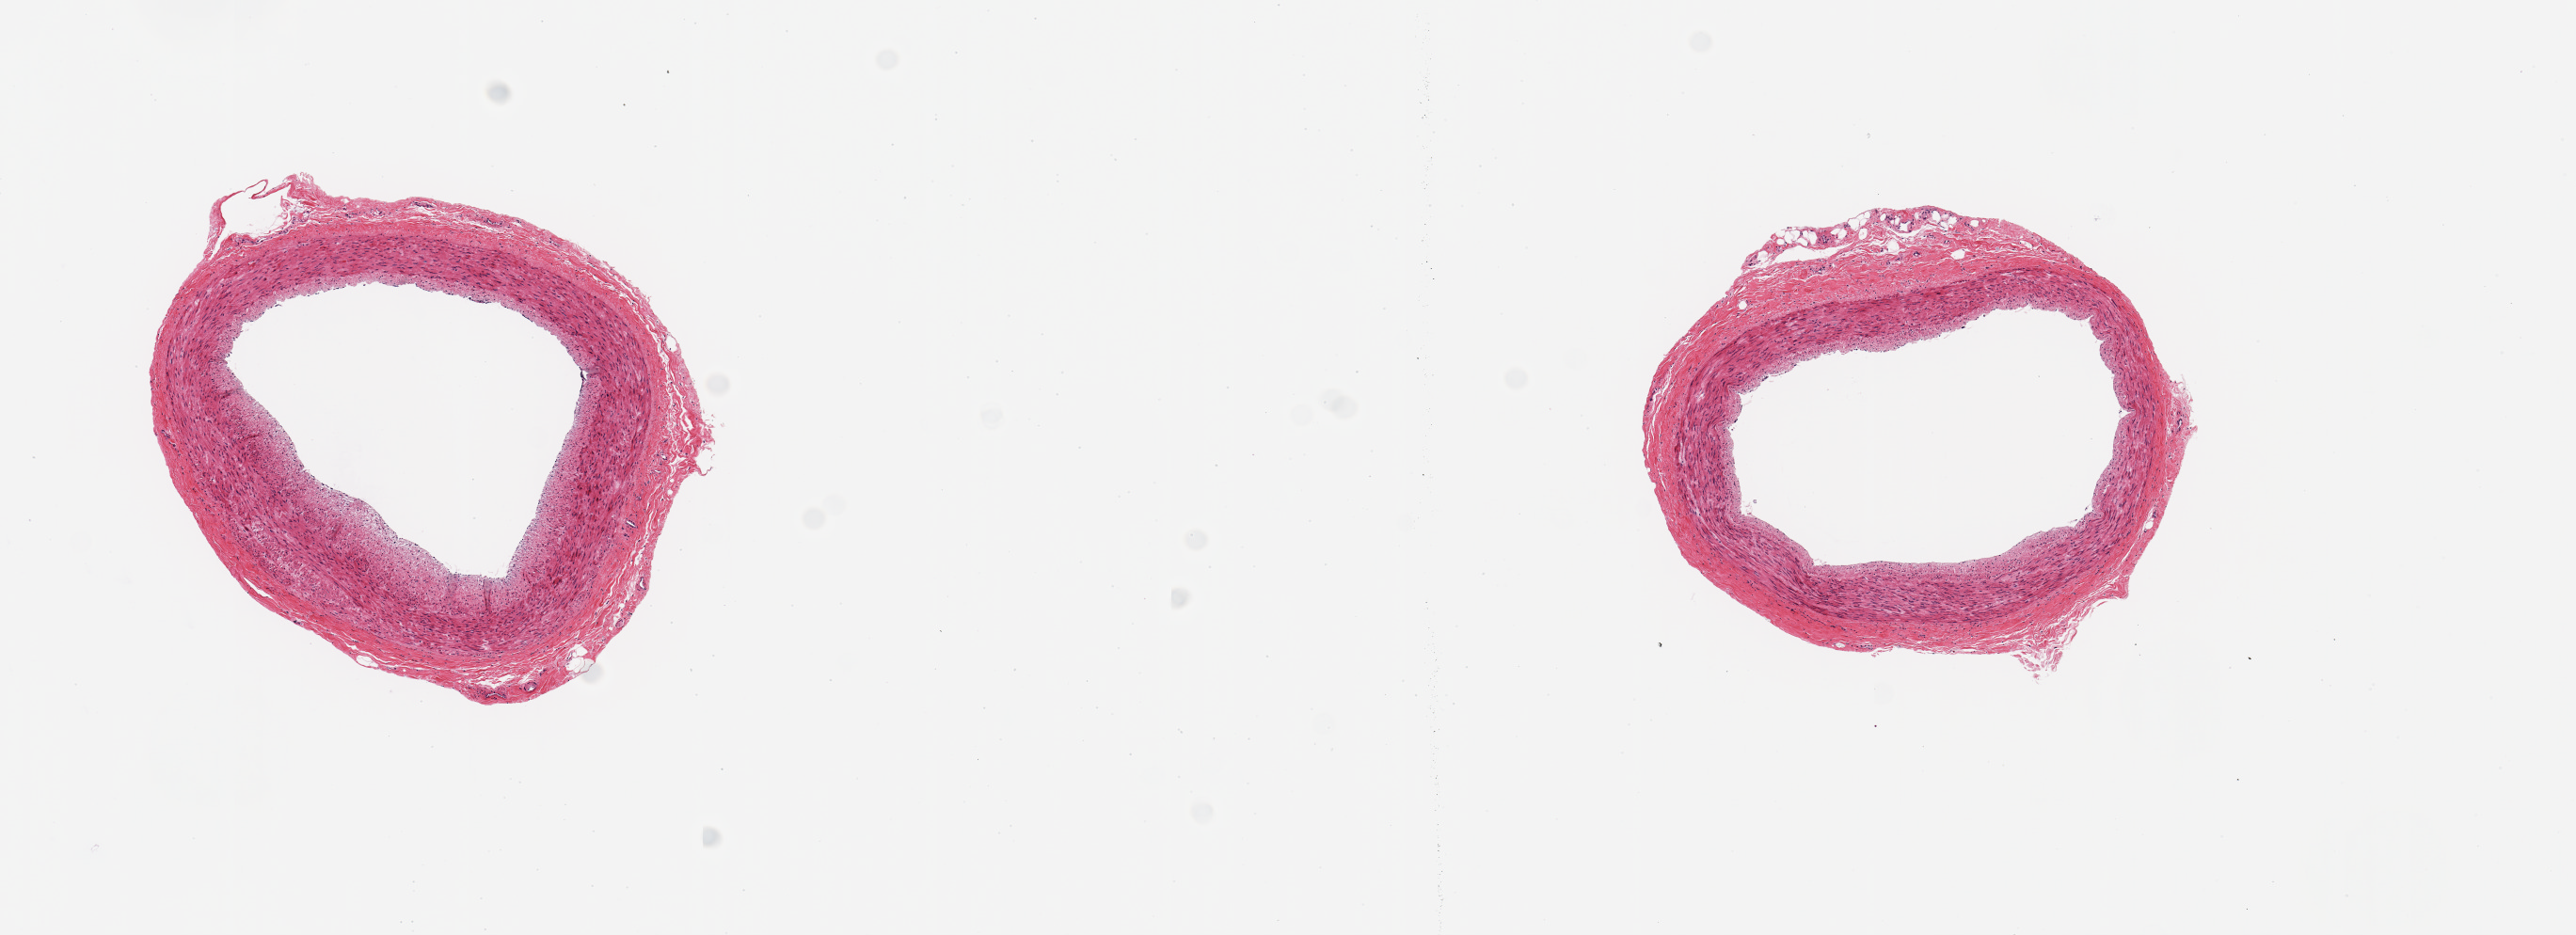
Digitized hematoxylin and eosin (H&E)-stained section, whole scanned area (about 10.8 x 3.9 mm) shown as a low-resolution overview. PAXgene-fixed paraffin-embedded (PFPE) section. Target tissue: coronary artery. Donor tissue sample. Donor sex: female.
Review note (as recorded): 2 pieces, 2.2 mm diameter; normal.